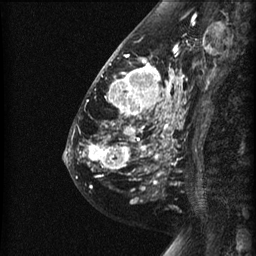
Breast MRI (dynamic contrast-enhanced), one sagittal slice. Position 23 of 60 along the scan axis. Dynamic contrast-enhanced series, image 2 of 3 at this slice position (ordered by acquisition). 1.5 T. TE 4.2 ms, TR 22.7 ms. 256 × 256 image matrix, field of view 180 × 180 mm. Patient: female, 48 years. Case-level facts recorded for this patient, not image findings: setting: breast cancer imaged before/during neoadjuvant chemotherapy; receptor status: triple-negative.
Outlined on this slice (semi-automatic segmentation, software-assisted and operator-edited):
- analysis volume of interest (the breast-tissue region the enhancement analysis was run in; not a lesion): bounding box (x1, y1, x2, y2) in pixels: (89, 27, 191, 180)
- tumour enhancement mask (voxels above the 90 % enhancement threshold inside the analysis volume of interest): (89, 55, 183, 177)